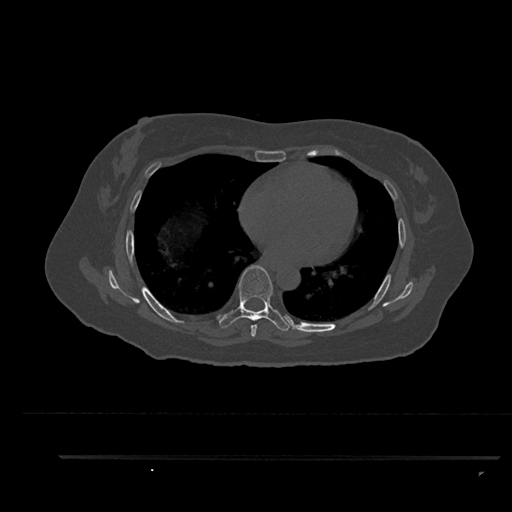
CT including the spine, one axial slice. Slice 517 of 797 in the series (ordered by position). Reconstruction kernel Br40s/3. 120 kVp. Bone window (W 1800 / L 400 HU). 0.5 mm slice thickness. 512 × 512 image matrix, field of view 408 × 408 mm. Patient: female, 44 years. Case-level facts recorded for this patient, not image findings: primary cancer: renal; vertebrae with lytic lesions (as recorded): L1.
Outlined on this slice (semi-automatic segmentation, software-assisted and operator-edited):
- T6 vertebra: bounding box [x1, y1, x2, y2] px = [251, 320, 257, 337]
- T7 vertebra: [219, 265, 293, 331]